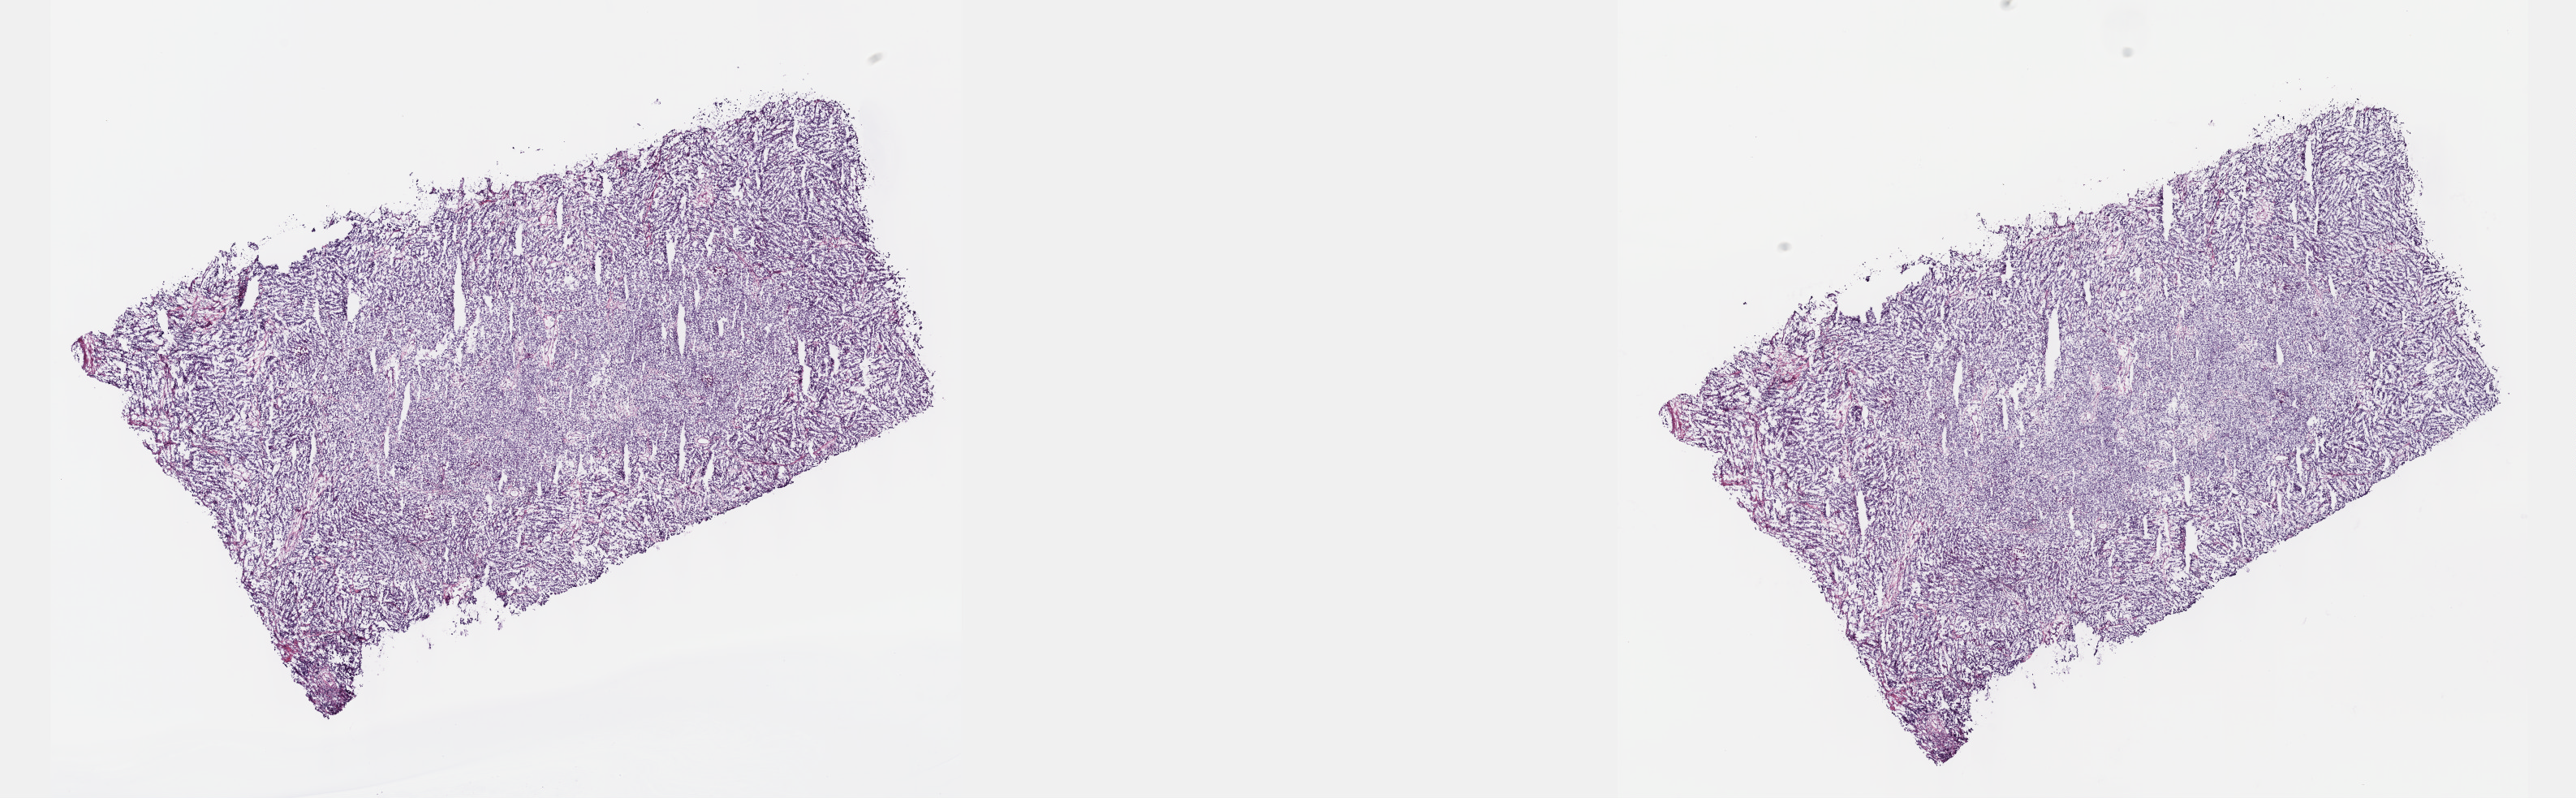
Digitized H&E tissue section (whole slide), whole scanned area (about 25.7 x 7.9 mm) shown as a low-resolution overview, frozen section from the top of the tissue portion, primary tumour sample from the testis. Male patient; age at initial diagnosis 37 years. Slide review estimates, as recorded: tumour cells 70%, tumour nuclei 70%, normal cells 0%, stromal cells 30%, necrosis 0%. Inflammatory infiltration, as recorded: lymphocyte infiltration 70%, monocyte infiltration 15%, neutrophil infiltration 5%.
AJCC pathologic stage: IS. Diagnosis: Seminoma, NOS.